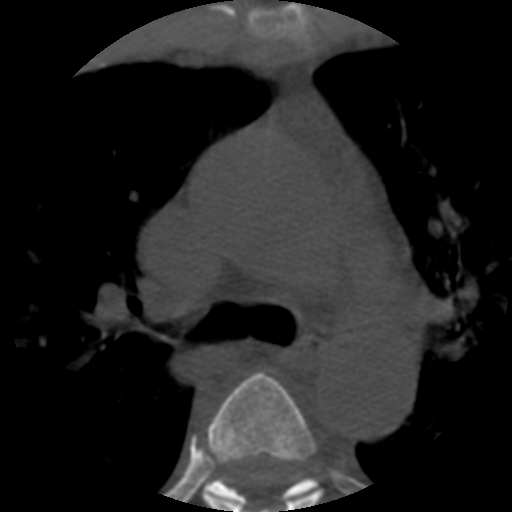
CT including the spine, one axial slice; position 388 of 508 along the scan axis; bone window (W 1800 / L 400 HU); 1.25 mm slice thickness; 512 × 512 image matrix. Patient age 57 years. From the clinical record (not read from this slice): primary cancer: prostate.
Structures marked on this image (semi-automatically segmented with operator editing):
- T4 vertebra: box from (x=202, y=372) to (x=322, y=512) px
- T5 vertebra: (x=205, y=476)–(x=319, y=504)